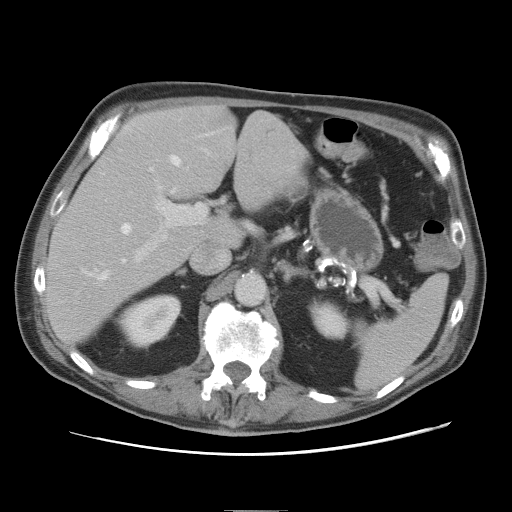
Contrast-enhanced abdominal CT, one axial slice; slice 46 of 89 in the series (ordered by position); 120 kVp; intravenous contrast given; soft-tissue window (W 400 / L 40 HU); 512 × 512 image matrix, field of view 375 × 375 mm. Male patient, age 69 years. Case-level facts recorded for this patient, not image findings: diagnosis: colorectal cancer liver metastases, imaged before liver resection; multiple liver metastases: no; largest metastasis: 8.5 cm; disease in both lobes: no.
Annotated regions visible in this slice (outlined manually by an expert reader):
- hepatic veins: bounding box <98,155,181,280> (left, top, right, bottom; pixels)
- liver: <46,108,302,342>
- planned liver remnant (the part of the liver to remain after resection): <46,108,240,342>
- portal vein (with intrahepatic branches): <135,149,209,262>